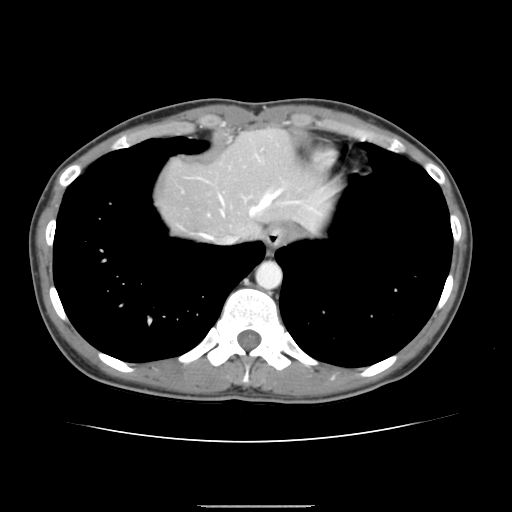
Contrast-enhanced abdominal CT, one axial slice; slice 129 of 150 in the series (ordered by position); 120 kVp; intravenous contrast given; soft-tissue window (W 400 / L 40 HU); 2.5 mm slice thickness; 512 × 512 image matrix, field of view 324 × 324 mm. Female patient, age 32 years. From the clinical record (not read from this slice): diagnosis: colorectal cancer liver metastases, imaged before liver resection; multiple liver metastases: yes; largest metastasis: 0.7 cm; disease in both lobes: no.
Outlined on this slice (outlined manually by an expert reader):
- hepatic veins: box from (x=202, y=189) to (x=282, y=243) px
- liver: (x=158, y=129)–(x=332, y=240)
- planned liver remnant (the part of the liver to remain after resection): (x=158, y=129)–(x=332, y=240)
- portal vein (with intrahepatic branches): (x=257, y=156)–(x=299, y=203)